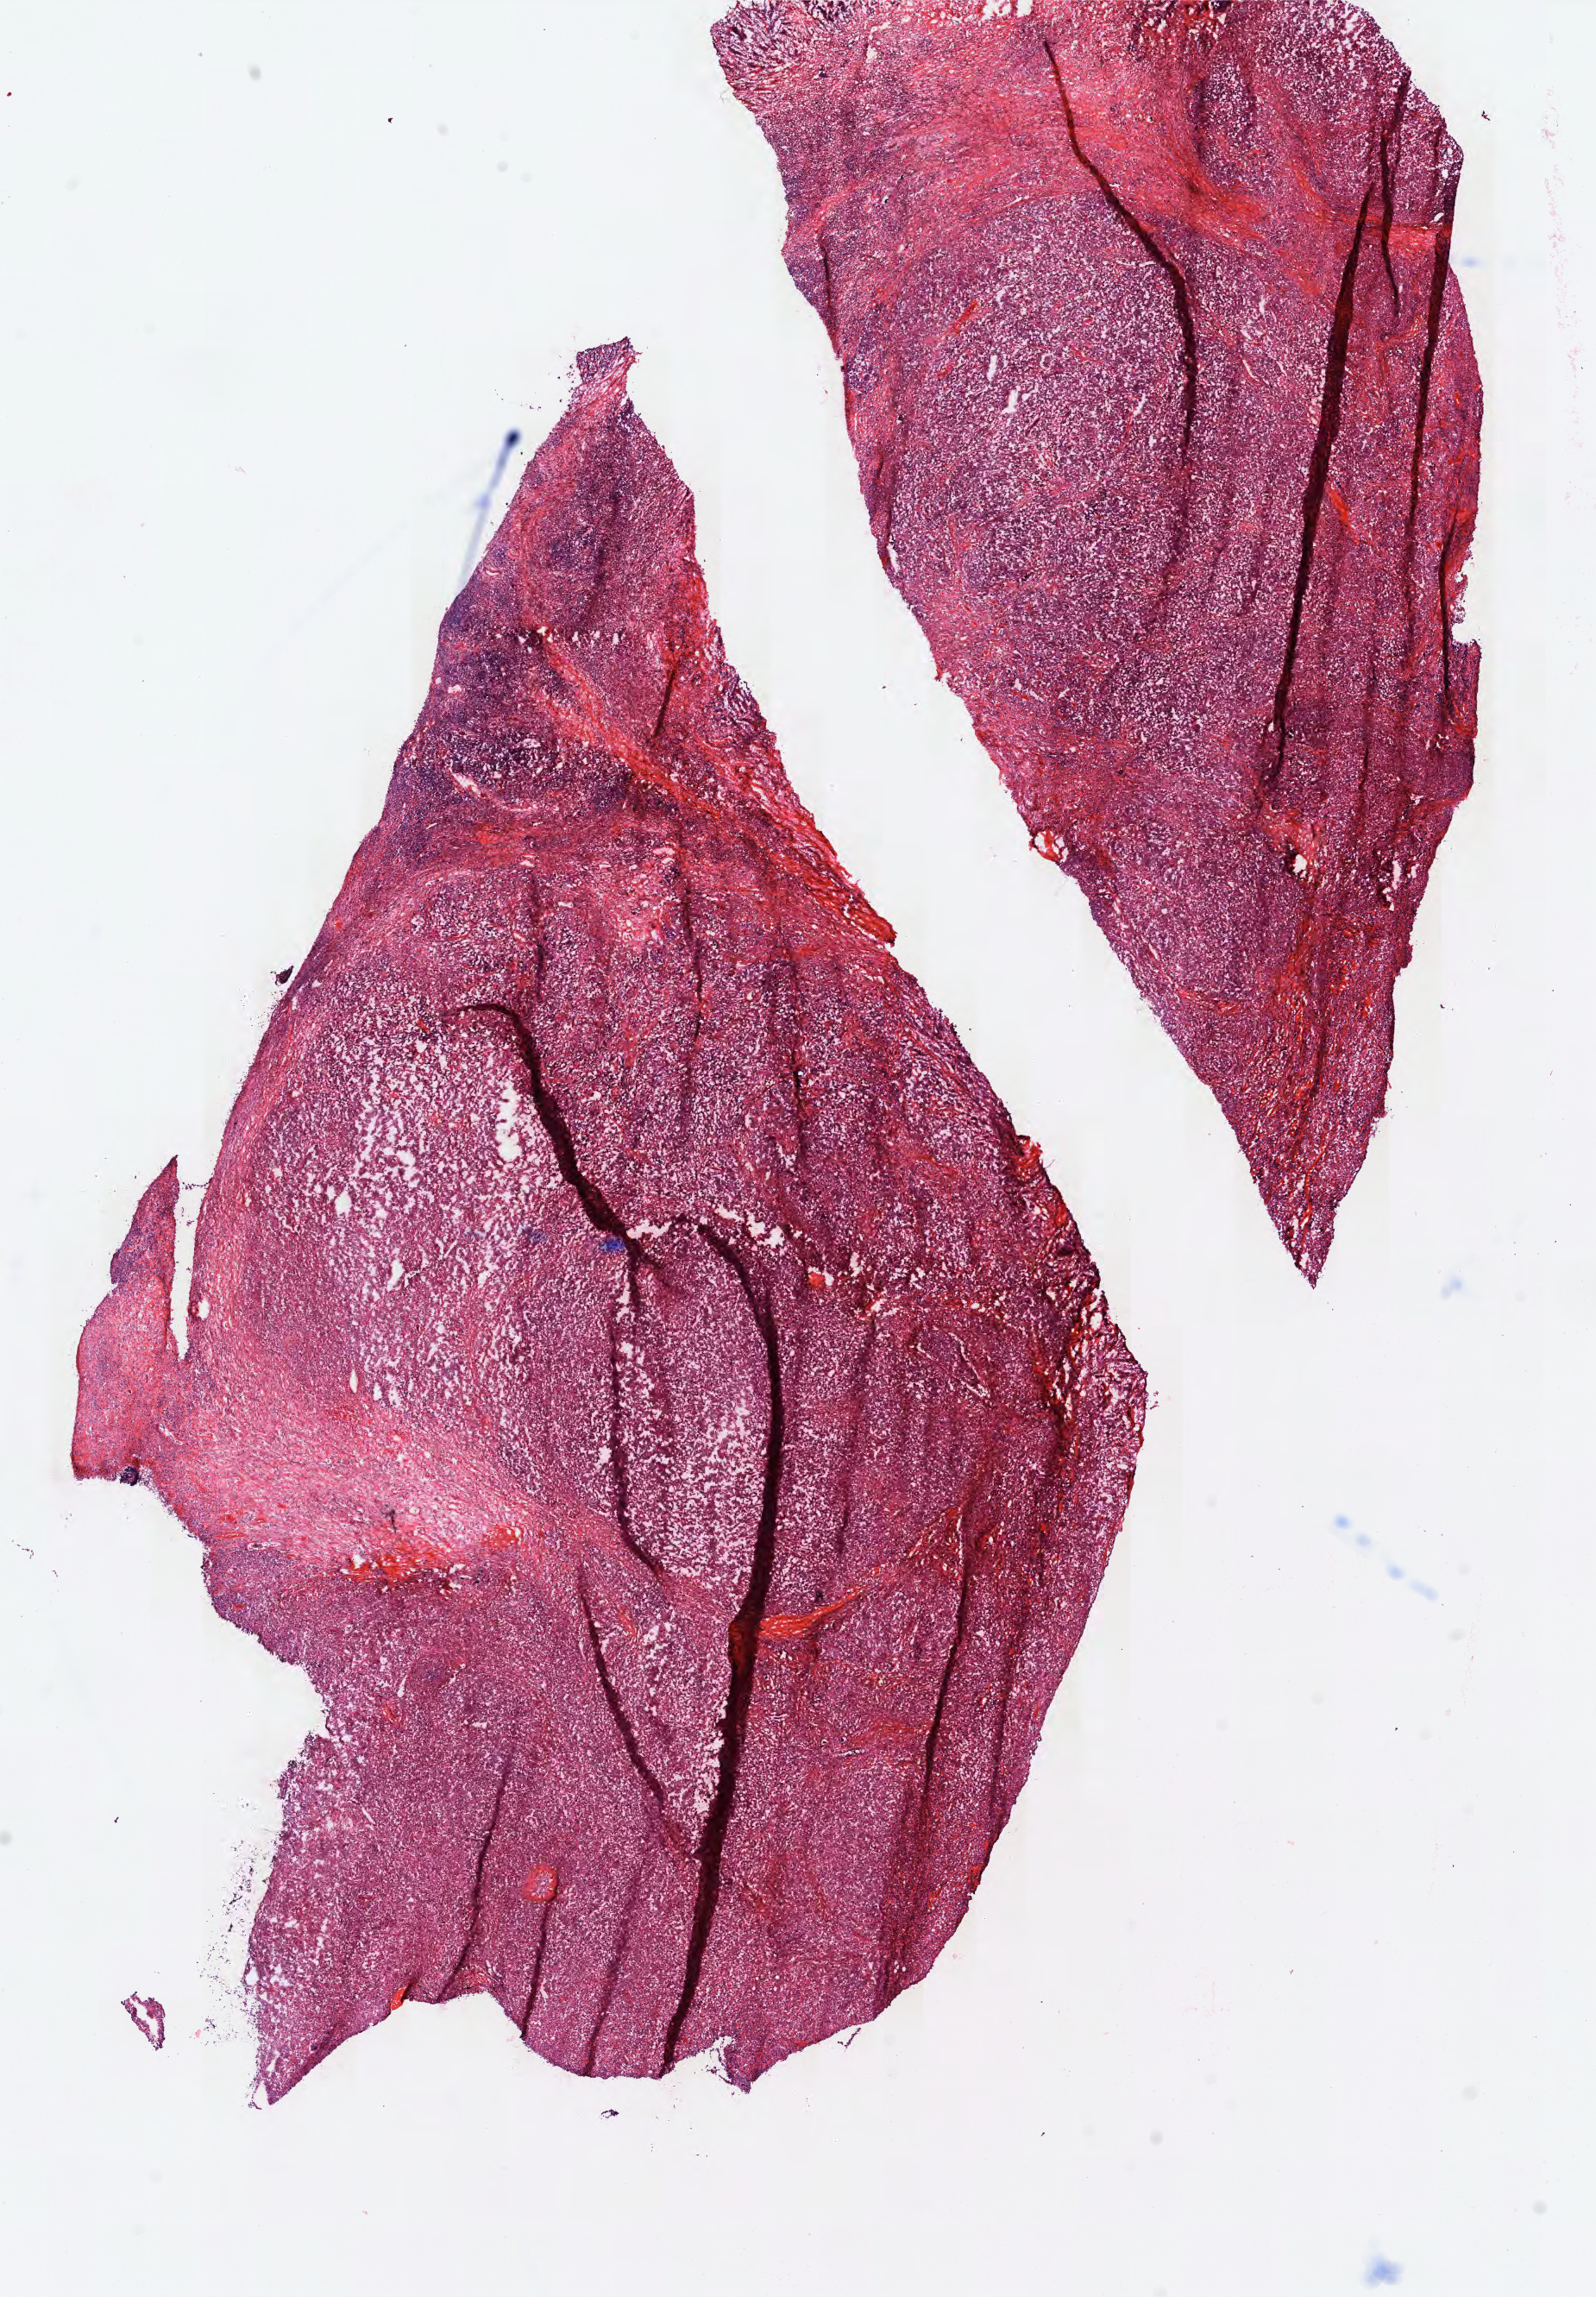
Digitized H&E-stained tissue section (whole slide), a low-resolution overview of the entire scanned area, about 13.8 x 19.8 mm. Formalin-fixed paraffin-embedded (FFPE) diagnostic section. Primary tumour sample from the lymphoid tissue. Patient: female, age at initial diagnosis 56 years.
Diagnosis: Diffuse large B-cell lymphoma, NOS (thyroid gland).